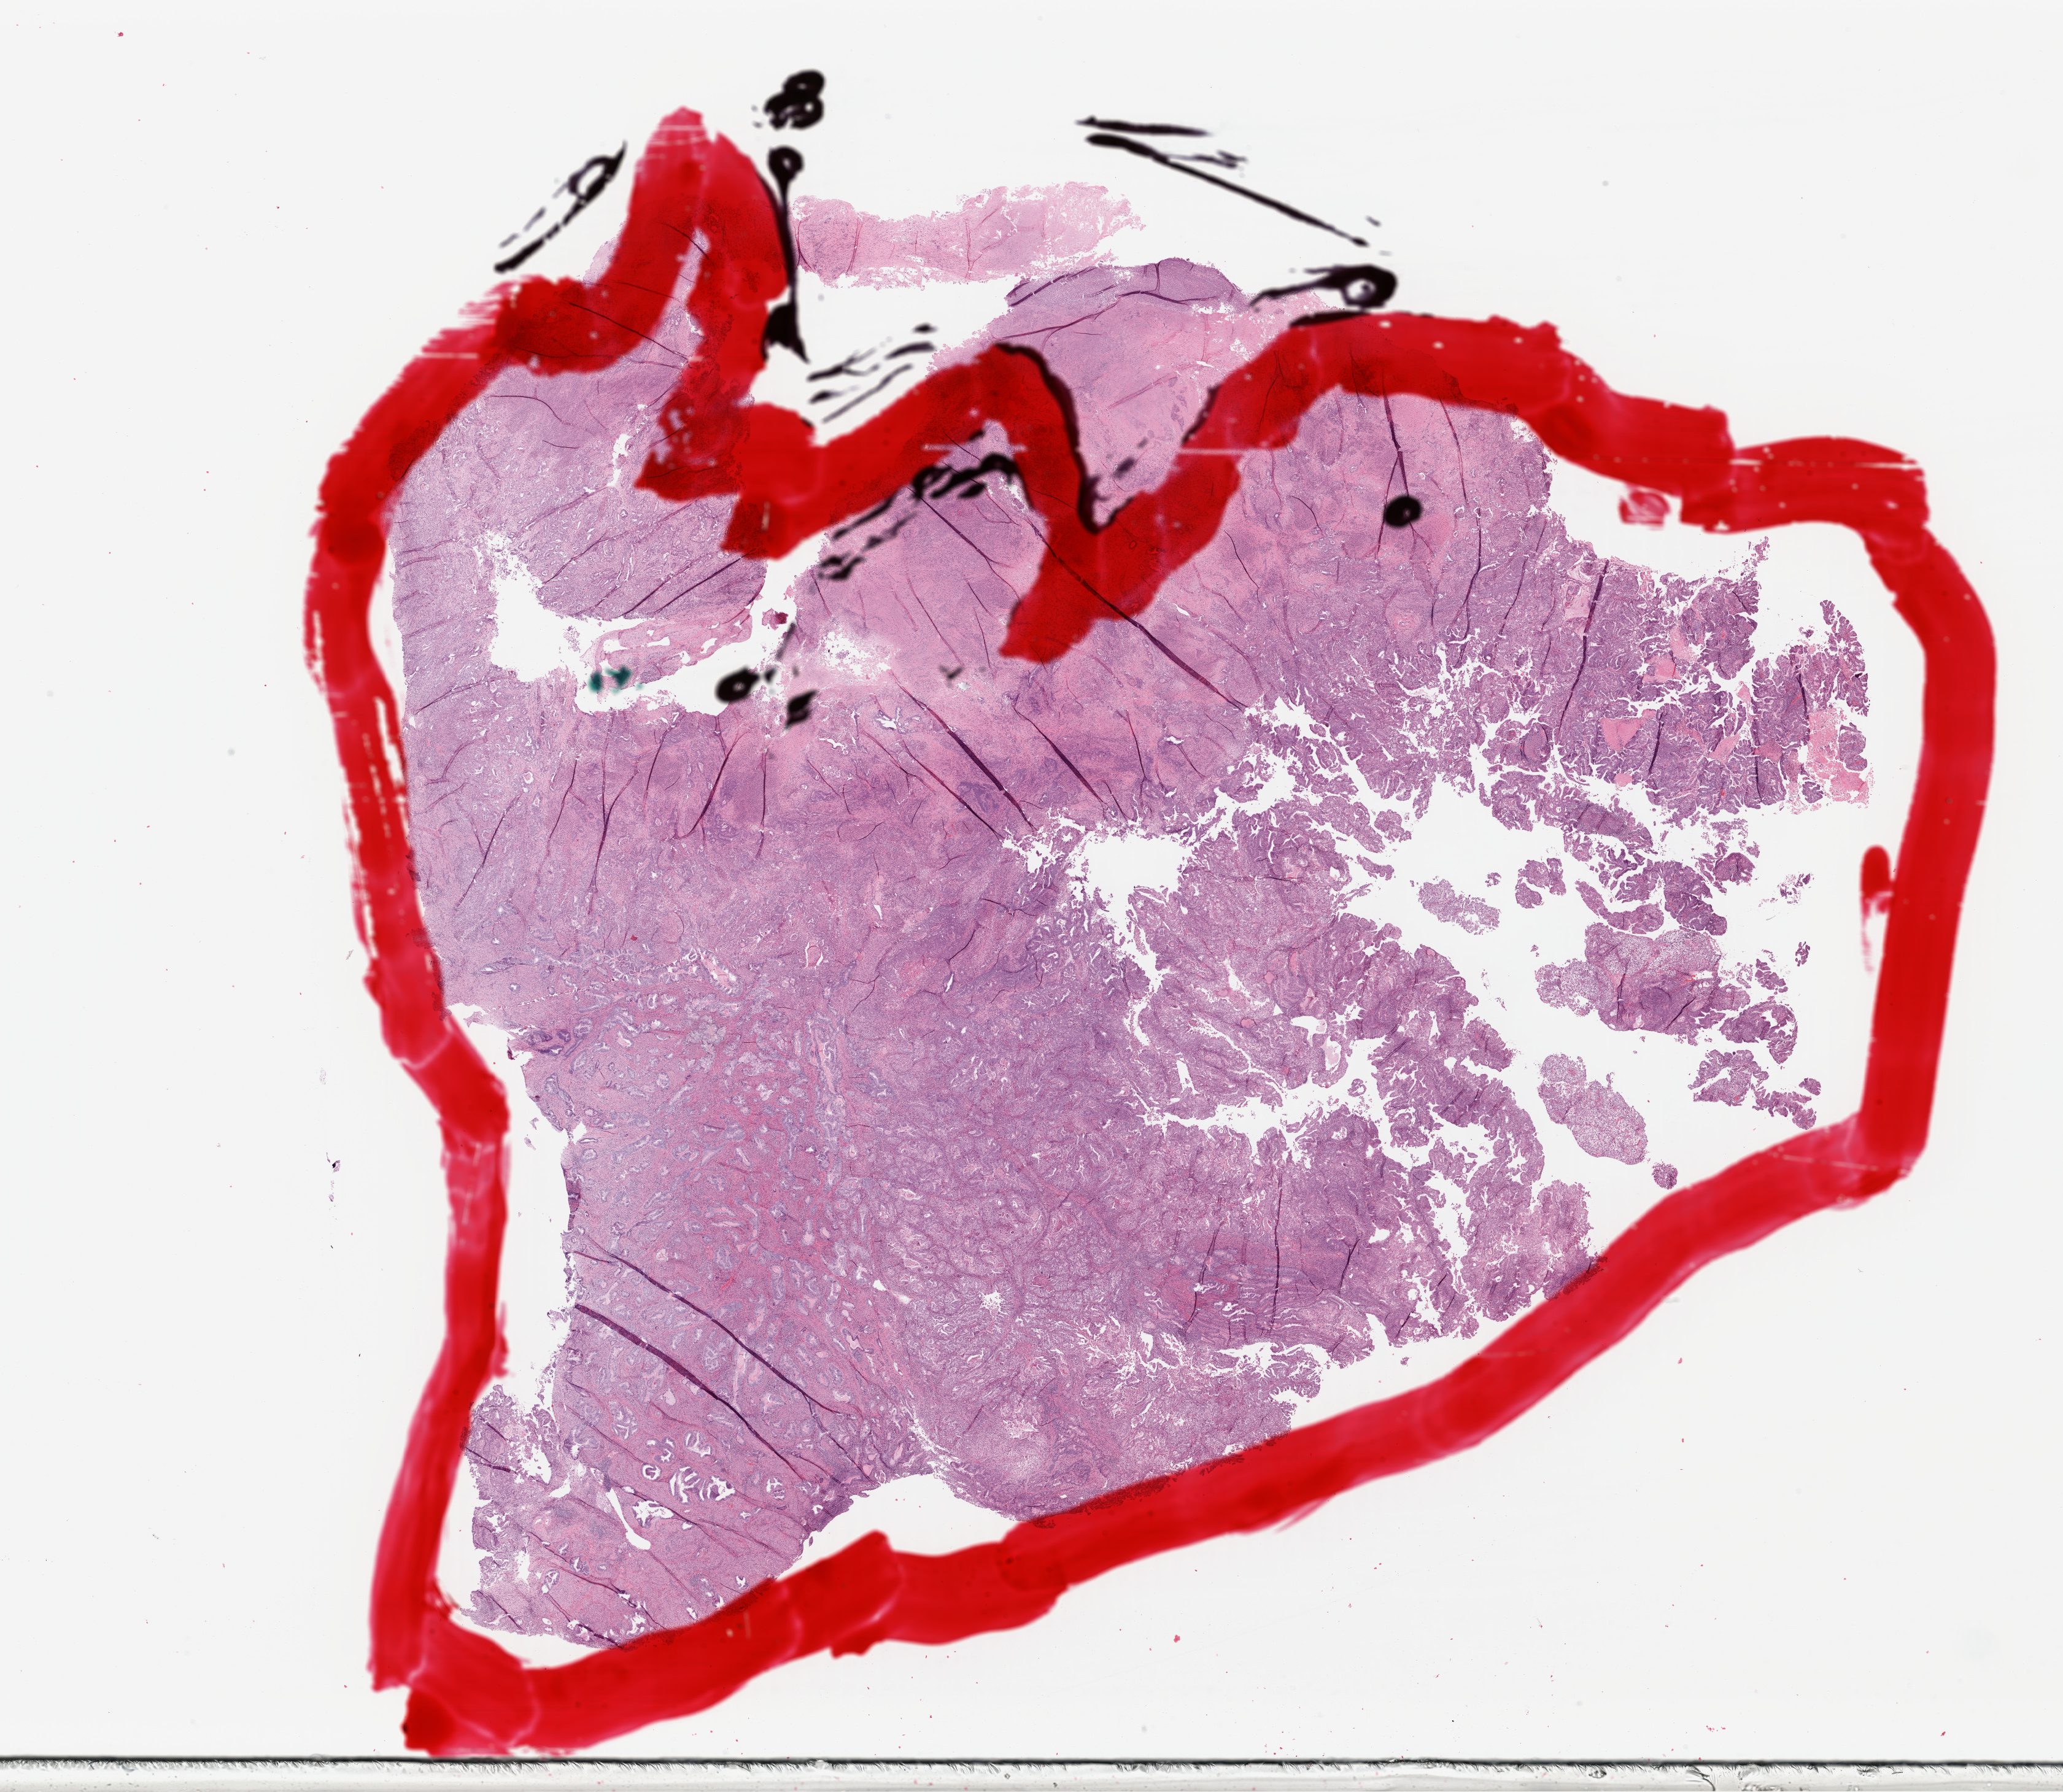
Digitized Hematoxylin and eosin (H&E) stained tissue section (whole slide) — low-resolution overview of the scanned area, about 26.4 x 23.0 mm (slide scanned at 40x). Formalin-fixed paraffin-embedded (FFPE) diagnostic section. Uterus, primary tumour sample. Patient: female, age at initial diagnosis 71 years.
Pathologic diagnosis: Endometrioid adenocarcinoma, NOS (endometrium).